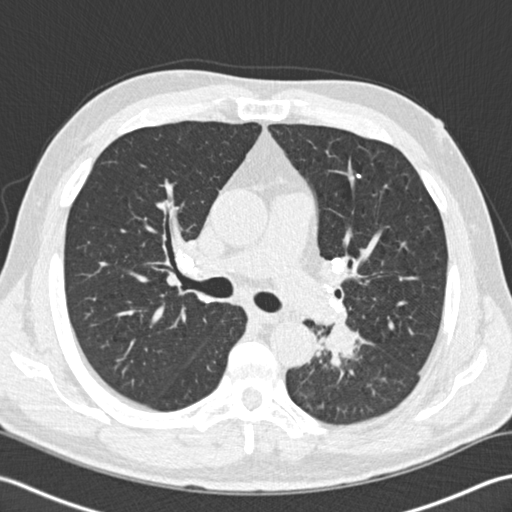
Low-dose screening chest CT, one axial slice; slice 108 of 170 in the series (ordered by position); lung window (W 1500 / L -600 HU); 2 mm slice thickness; 512 × 512 image matrix.
Outlined on this slice (manually delineated by an expert):
- lesion 1 (tumor, lower lobe of left lung): bounding box (x1, y1, x2, y2) in pixels: (324, 322, 359, 359)